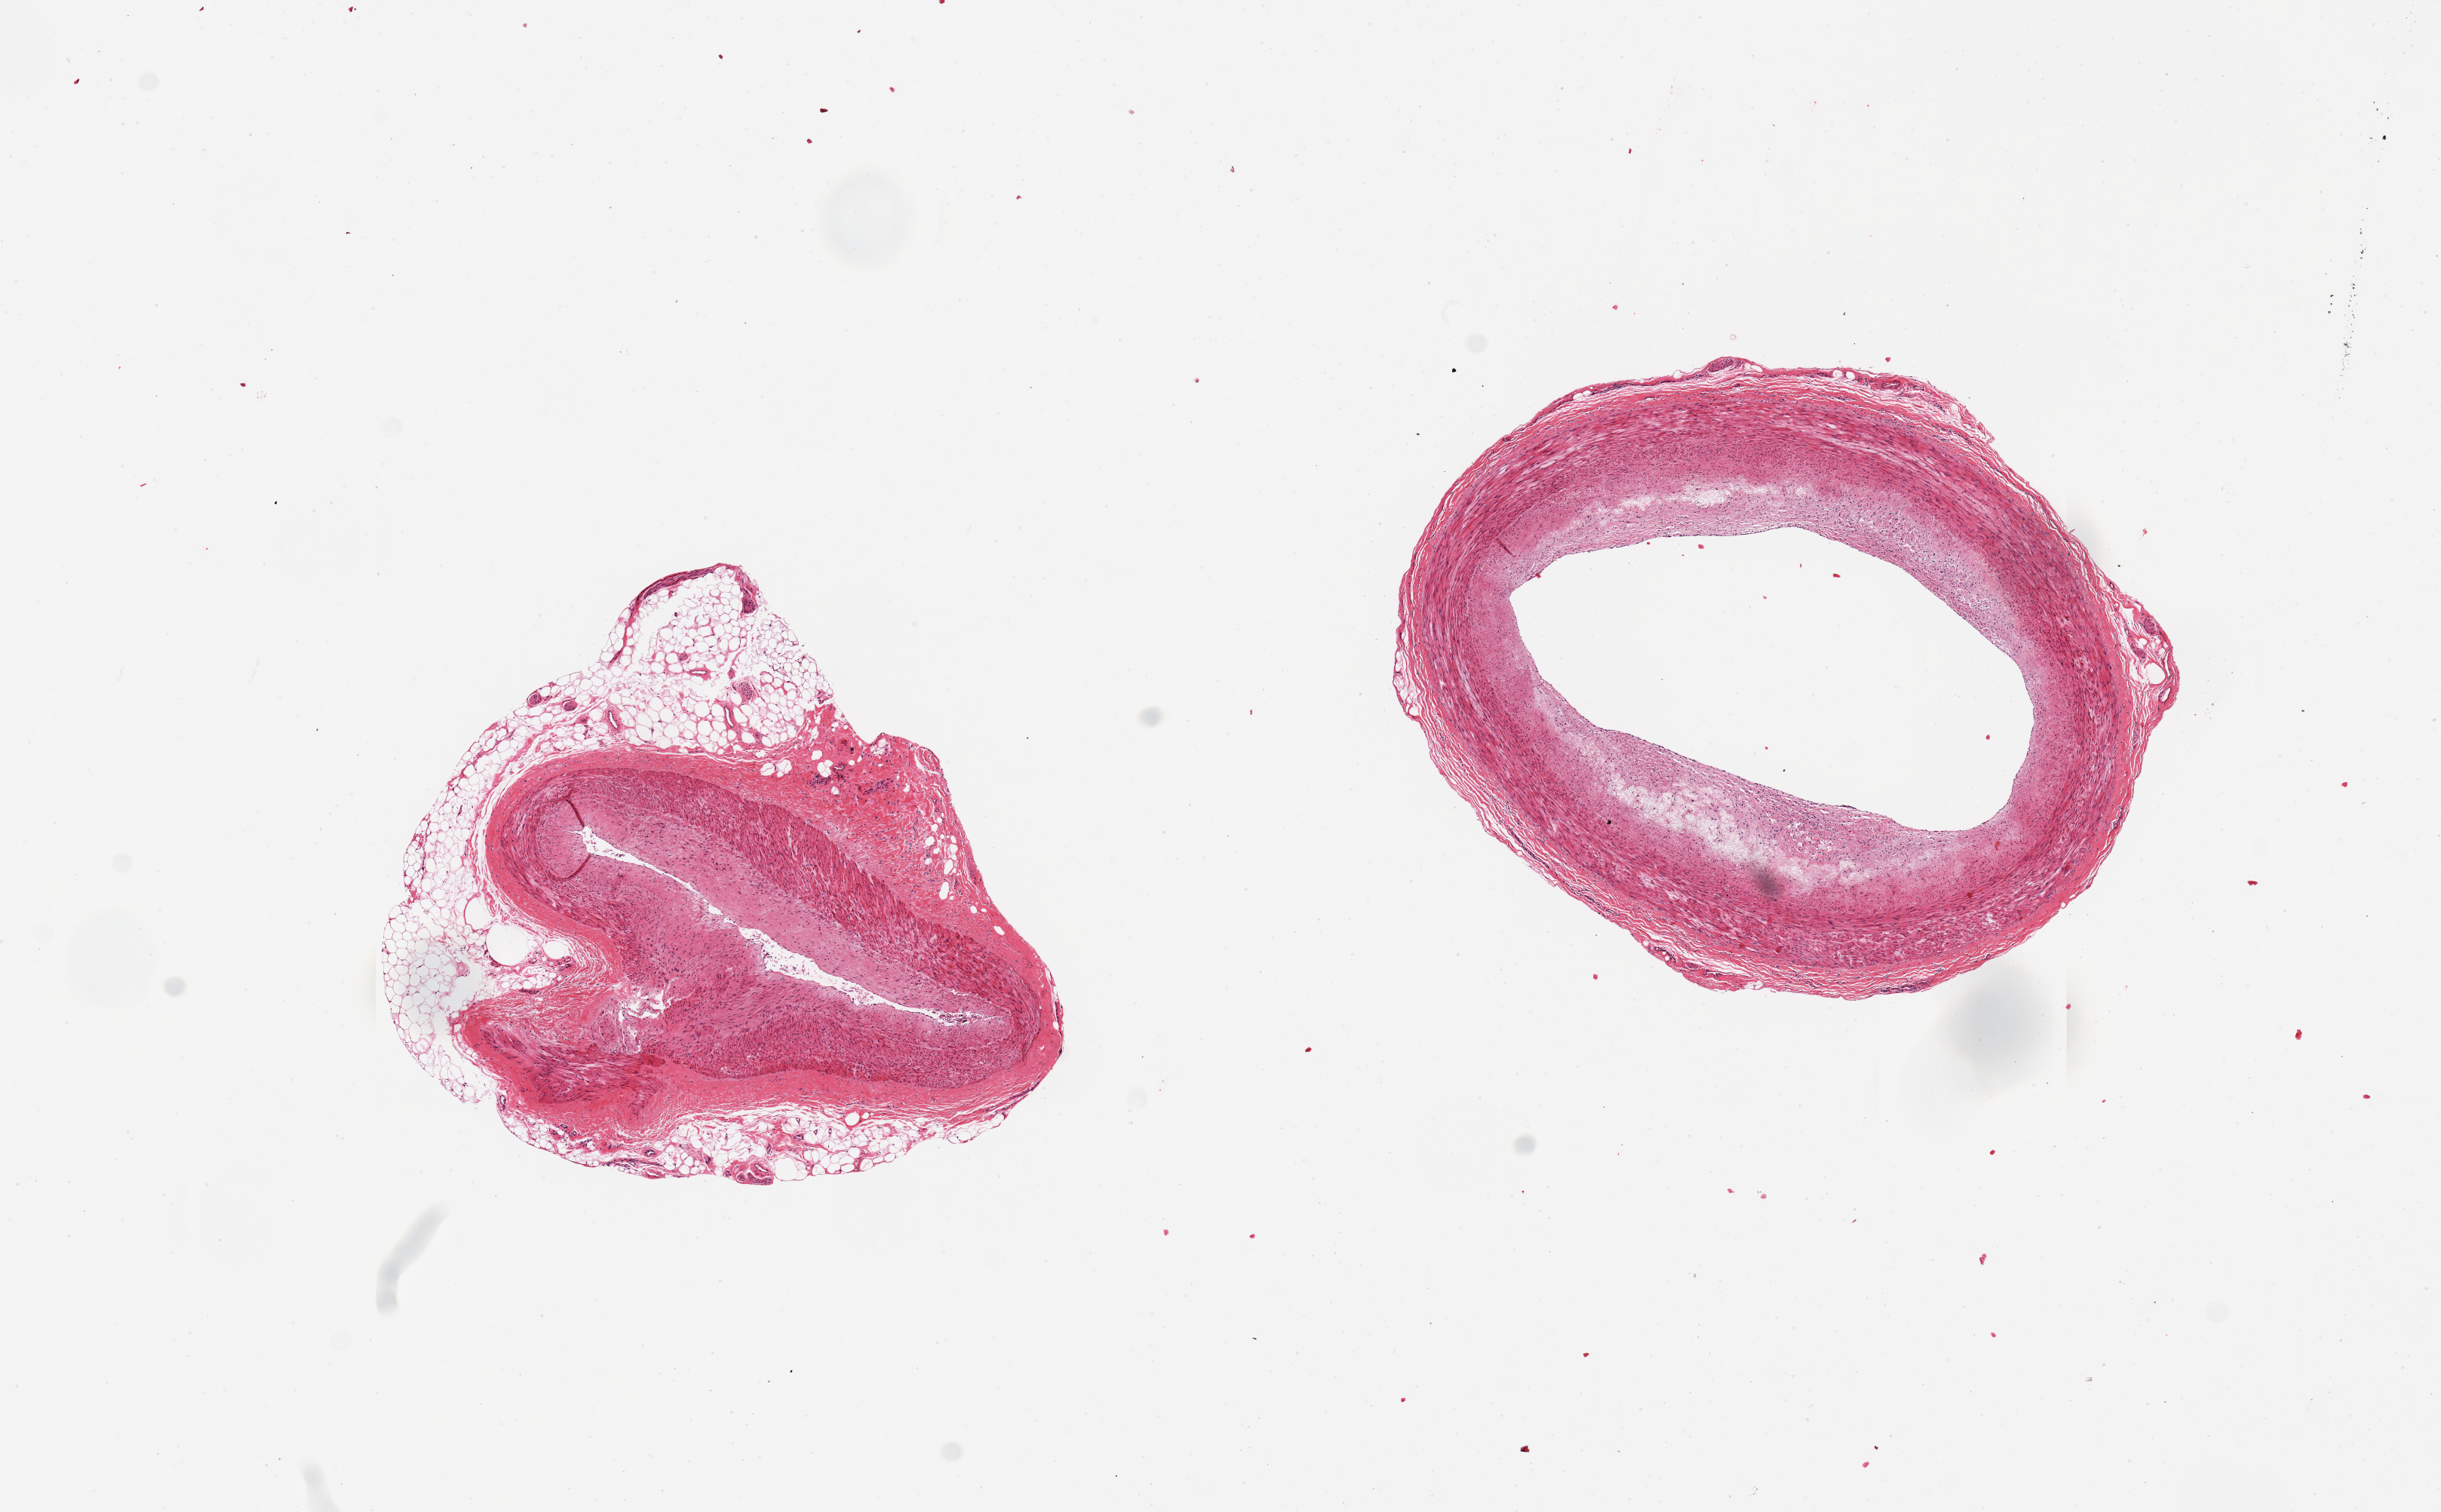
Whole-slide image, haematoxylin and eosin stain, a low-resolution overview of the entire scanned area, about 12.8 x 7.9 mm (slide scanned at 20x), PAXgene-fixed, paraffin-embedded tissue, target tissue: coronary artery, tissue donor sample. Male donor.
Reviewer comment on this tissue sample: 2 pieces, atheromatous plaque with foamy macrophages and cholesterol clefts, one piece has partial rim of fat (30%).